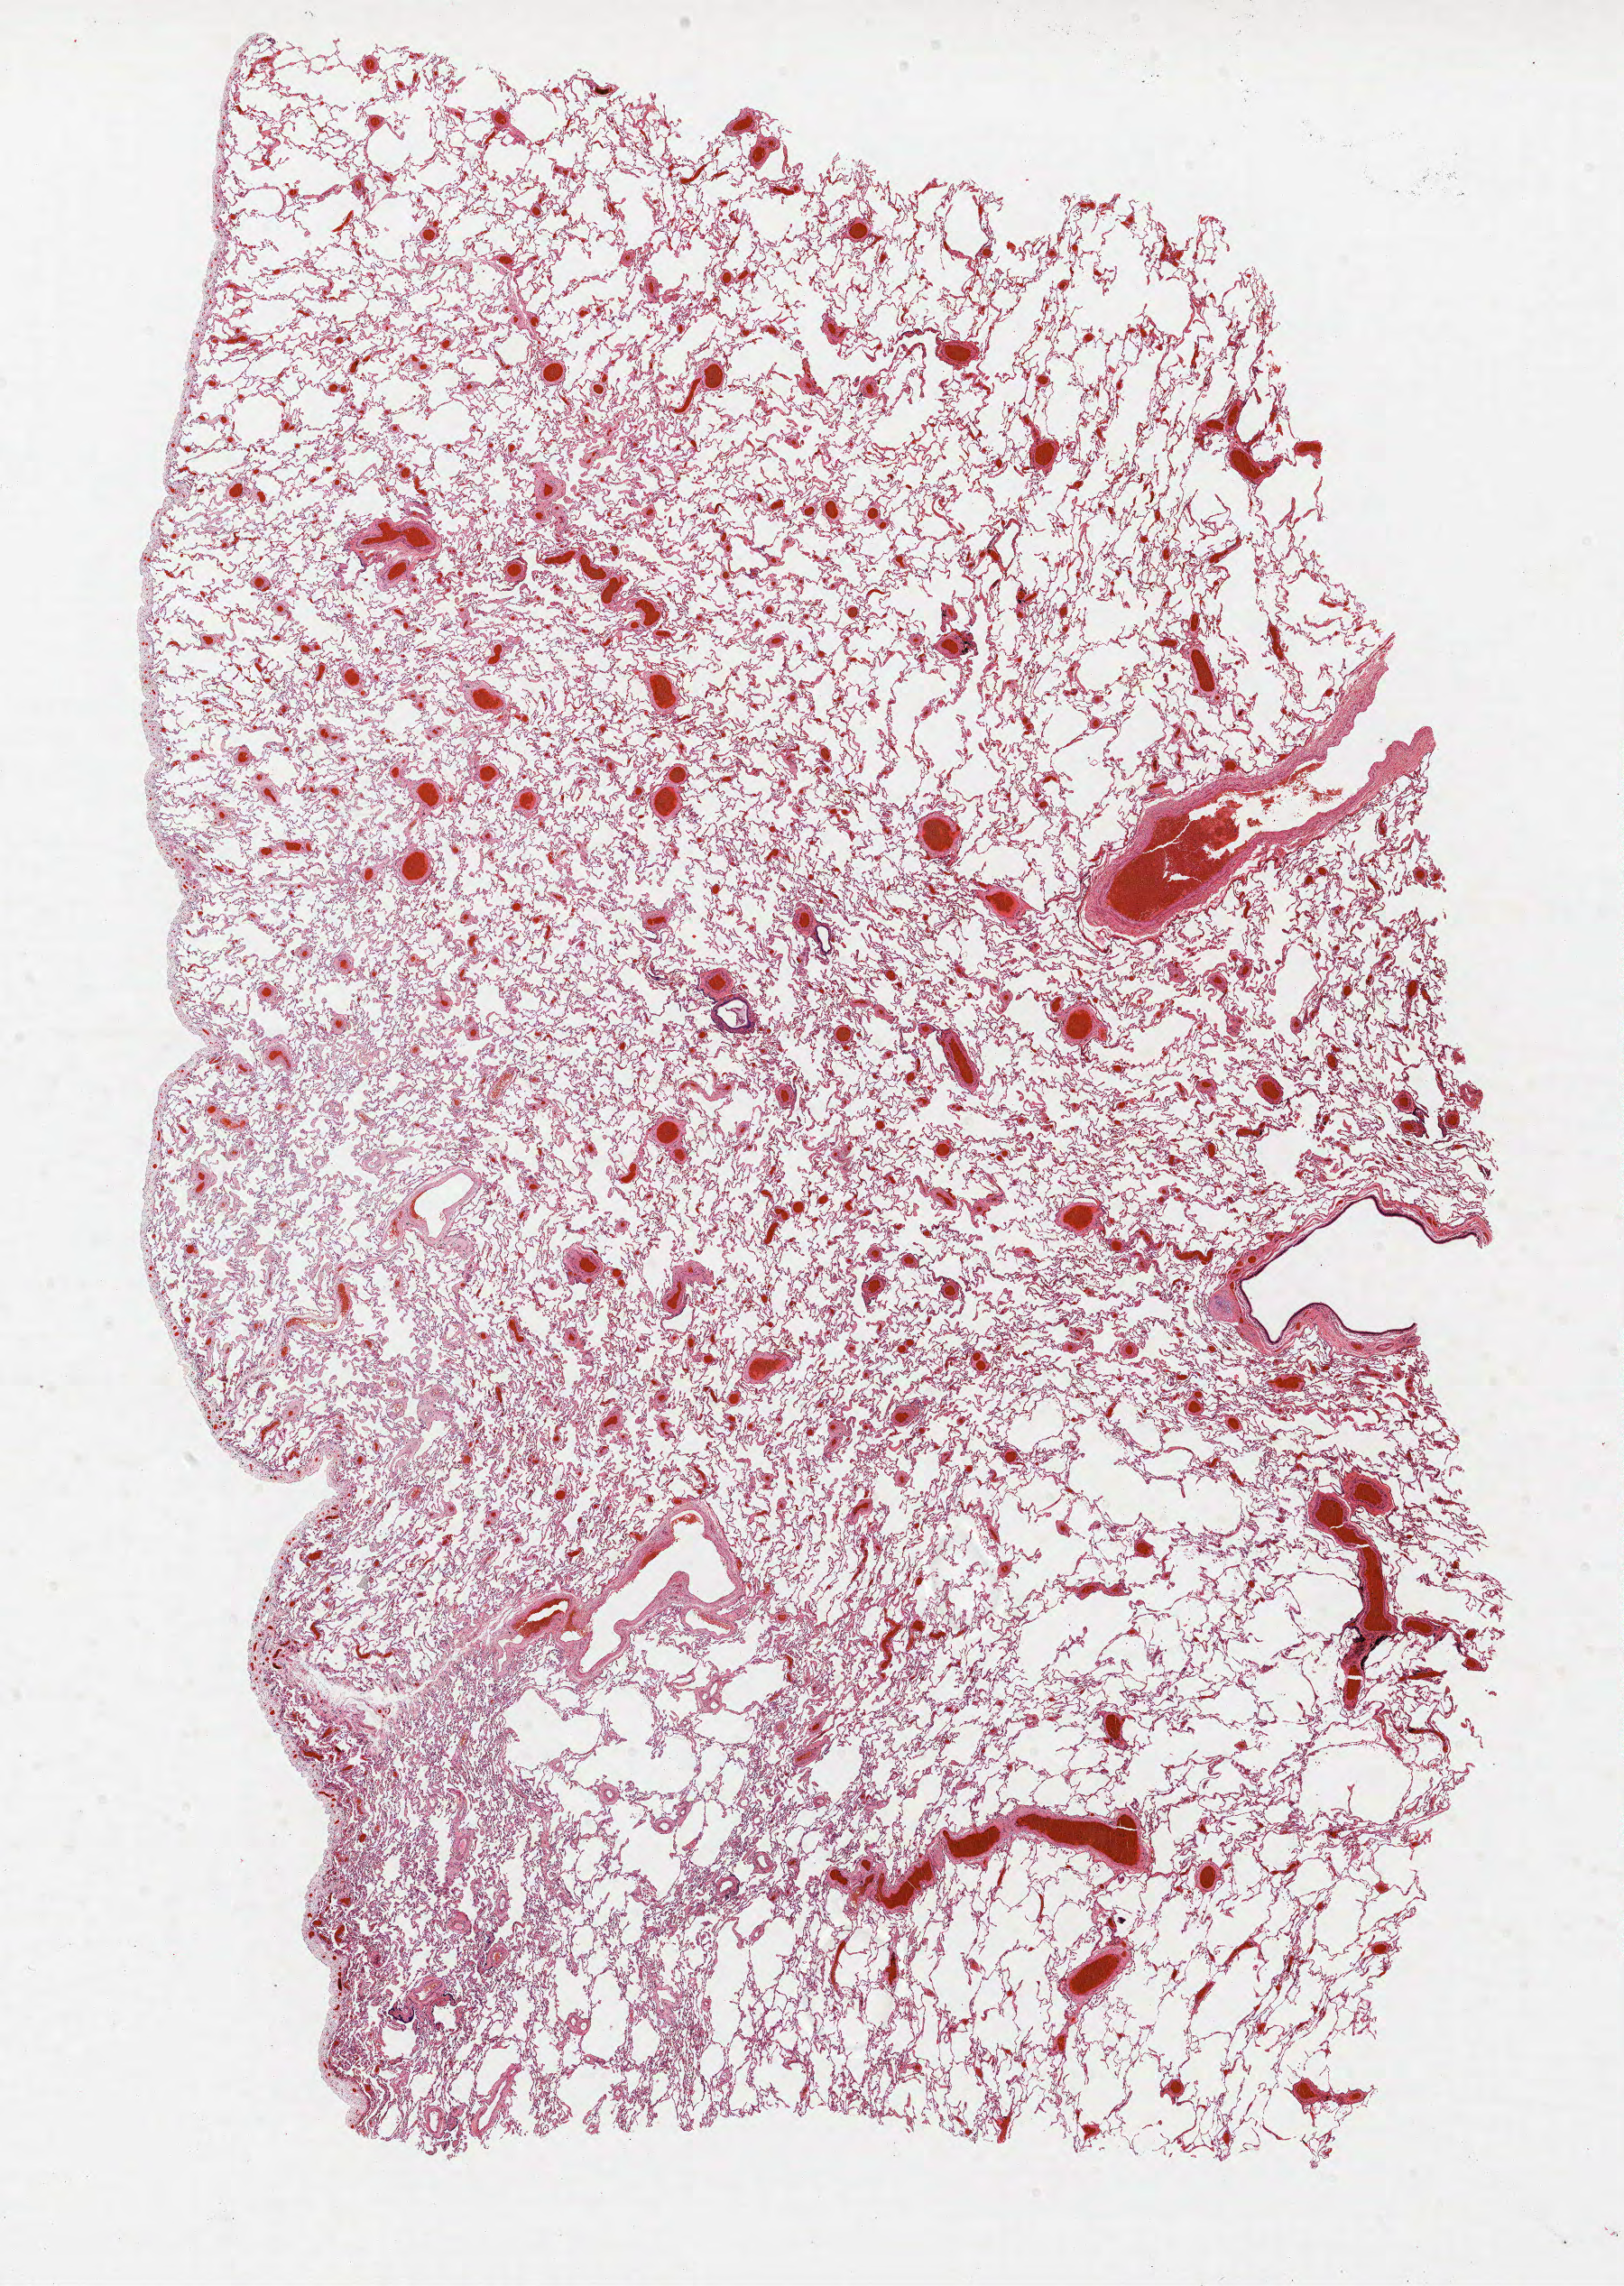
H&E-stained whole-slide image — whole scanned area (about 14.4 x 20.3 mm) shown as a low-resolution overview. Formalin-fixed paraffin-embedded (FFPE) section. Lung. Female patient, aged 67 at enrolment. Current smoker at enrolment. Grade: poorly differentiated (G3).
- stage (AJCC 6th edition): IB
- tumour size (pathology): 50 mm
- participant's lung-cancer diagnosis: Squamous cell carcinoma, NOS
- primary tumour location (clinical record): left lower lobe